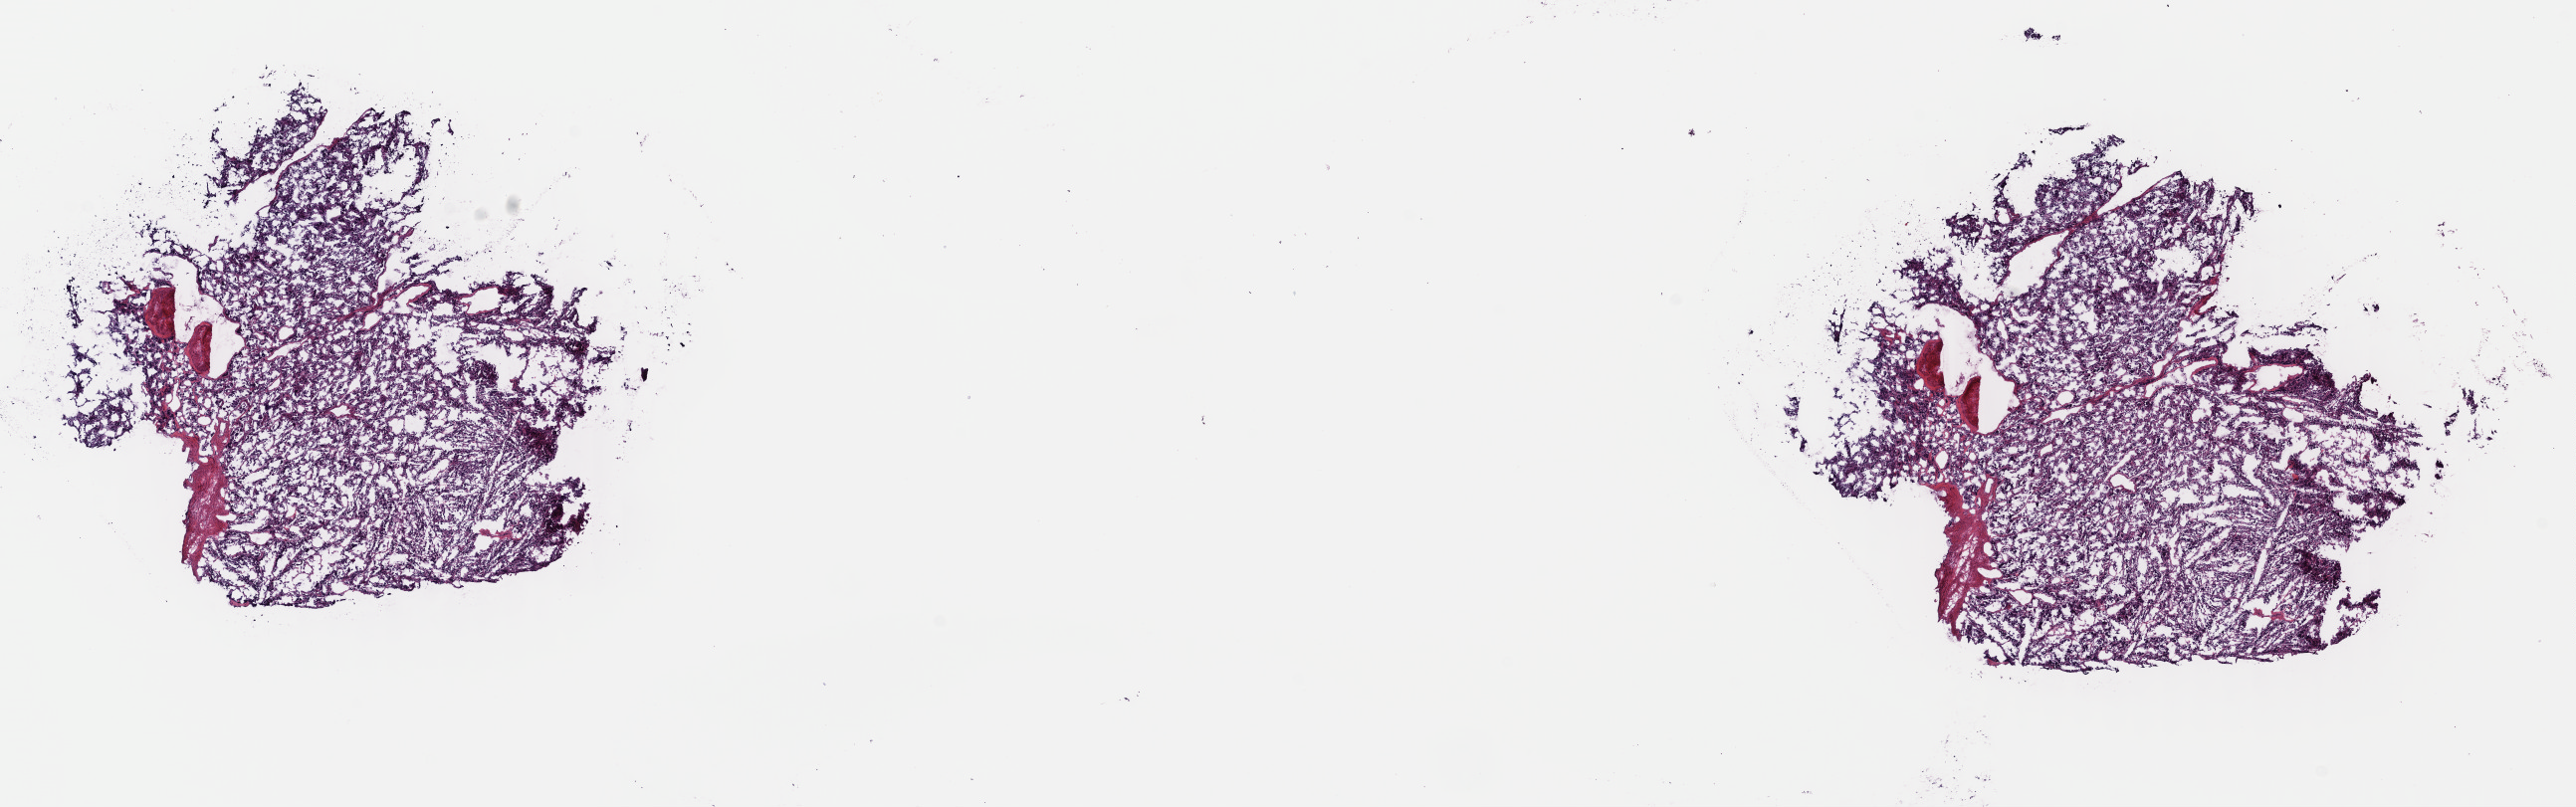
Whole-slide histology image, Hematoxylin and eosin (H&E) stained — shown as a low-resolution overview of the whole scanned area (about 20.3 x 6.4 mm, acquisition: 40x scan), frozen section, retroperitoneum and peritoneum, primary tumour sample. Patient: female, age at initial diagnosis 35 years. Pathologist review of this section (percent, as recorded): tumour cells 97%, tumour nuclei 95%.
Diagnosis: Extra-adrenal paraganglioma, NOS.